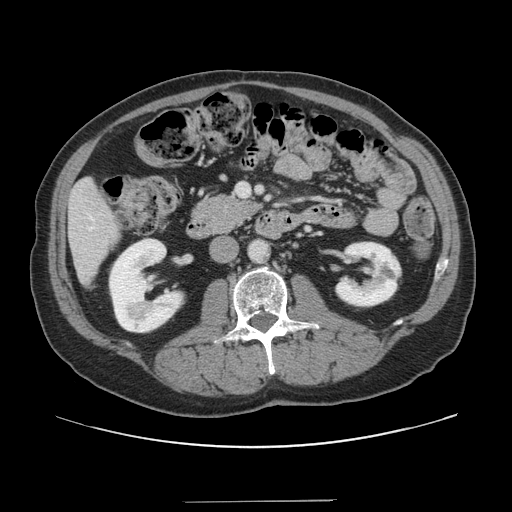
Contrast-enhanced abdominal CT, one axial slice. 120 kVp. Intravenous contrast given. Soft-tissue window (W 400 / L 40 HU). 2.5 mm slice thickness. 512 × 512 image matrix, field of view 399 × 399 mm. Male patient, age 63 years. Case-level facts recorded for this patient, not image findings: diagnosis: colorectal cancer liver metastases, imaged before liver resection; multiple liver metastases: no; largest metastasis: 2.1 cm.
Annotated regions visible in this slice (expert manual segmentation):
- hepatic veins: bounding box [x1, y1, x2, y2] px = [90, 218, 92, 230]
- liver: [69, 180, 120, 283]
- planned liver remnant (the part of the liver to remain after resection): [69, 180, 120, 283]
- portal vein (with intrahepatic branches): [237, 183, 250, 197]